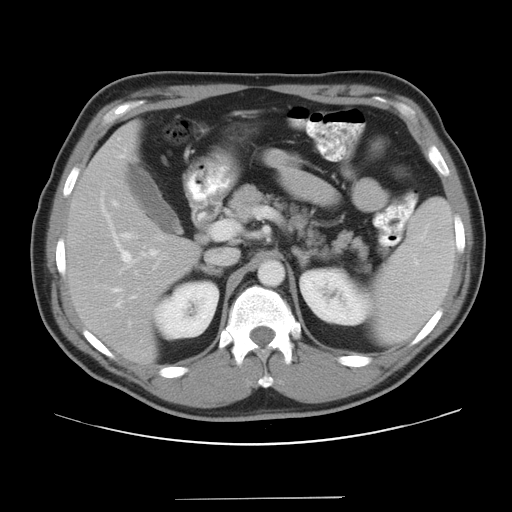
Contrast-enhanced abdominal CT, one axial slice; slice 23 of 37 in the series (ordered by position); 120 kVp; intravenous contrast given; soft-tissue window (W 400 / L 40 HU); 7.5 mm slice thickness; 512 × 512 image matrix, field of view 400 × 400 mm. Male patient, age 46 years. Case-level facts recorded for this patient, not image findings: diagnosis: colorectal cancer liver metastases, imaged before liver resection; multiple liver metastases: yes; largest metastasis: 1 cm; disease in both lobes: no.
Annotated regions visible in this slice (expert manual segmentation):
- hepatic veins: bounding box (x1, y1, x2, y2) in pixels: (112, 232, 135, 292)
- liver: (68, 125, 198, 359)
- planned liver remnant (the part of the liver to remain after resection): (68, 125, 198, 359)
- portal vein (with intrahepatic branches): (150, 249, 157, 255)